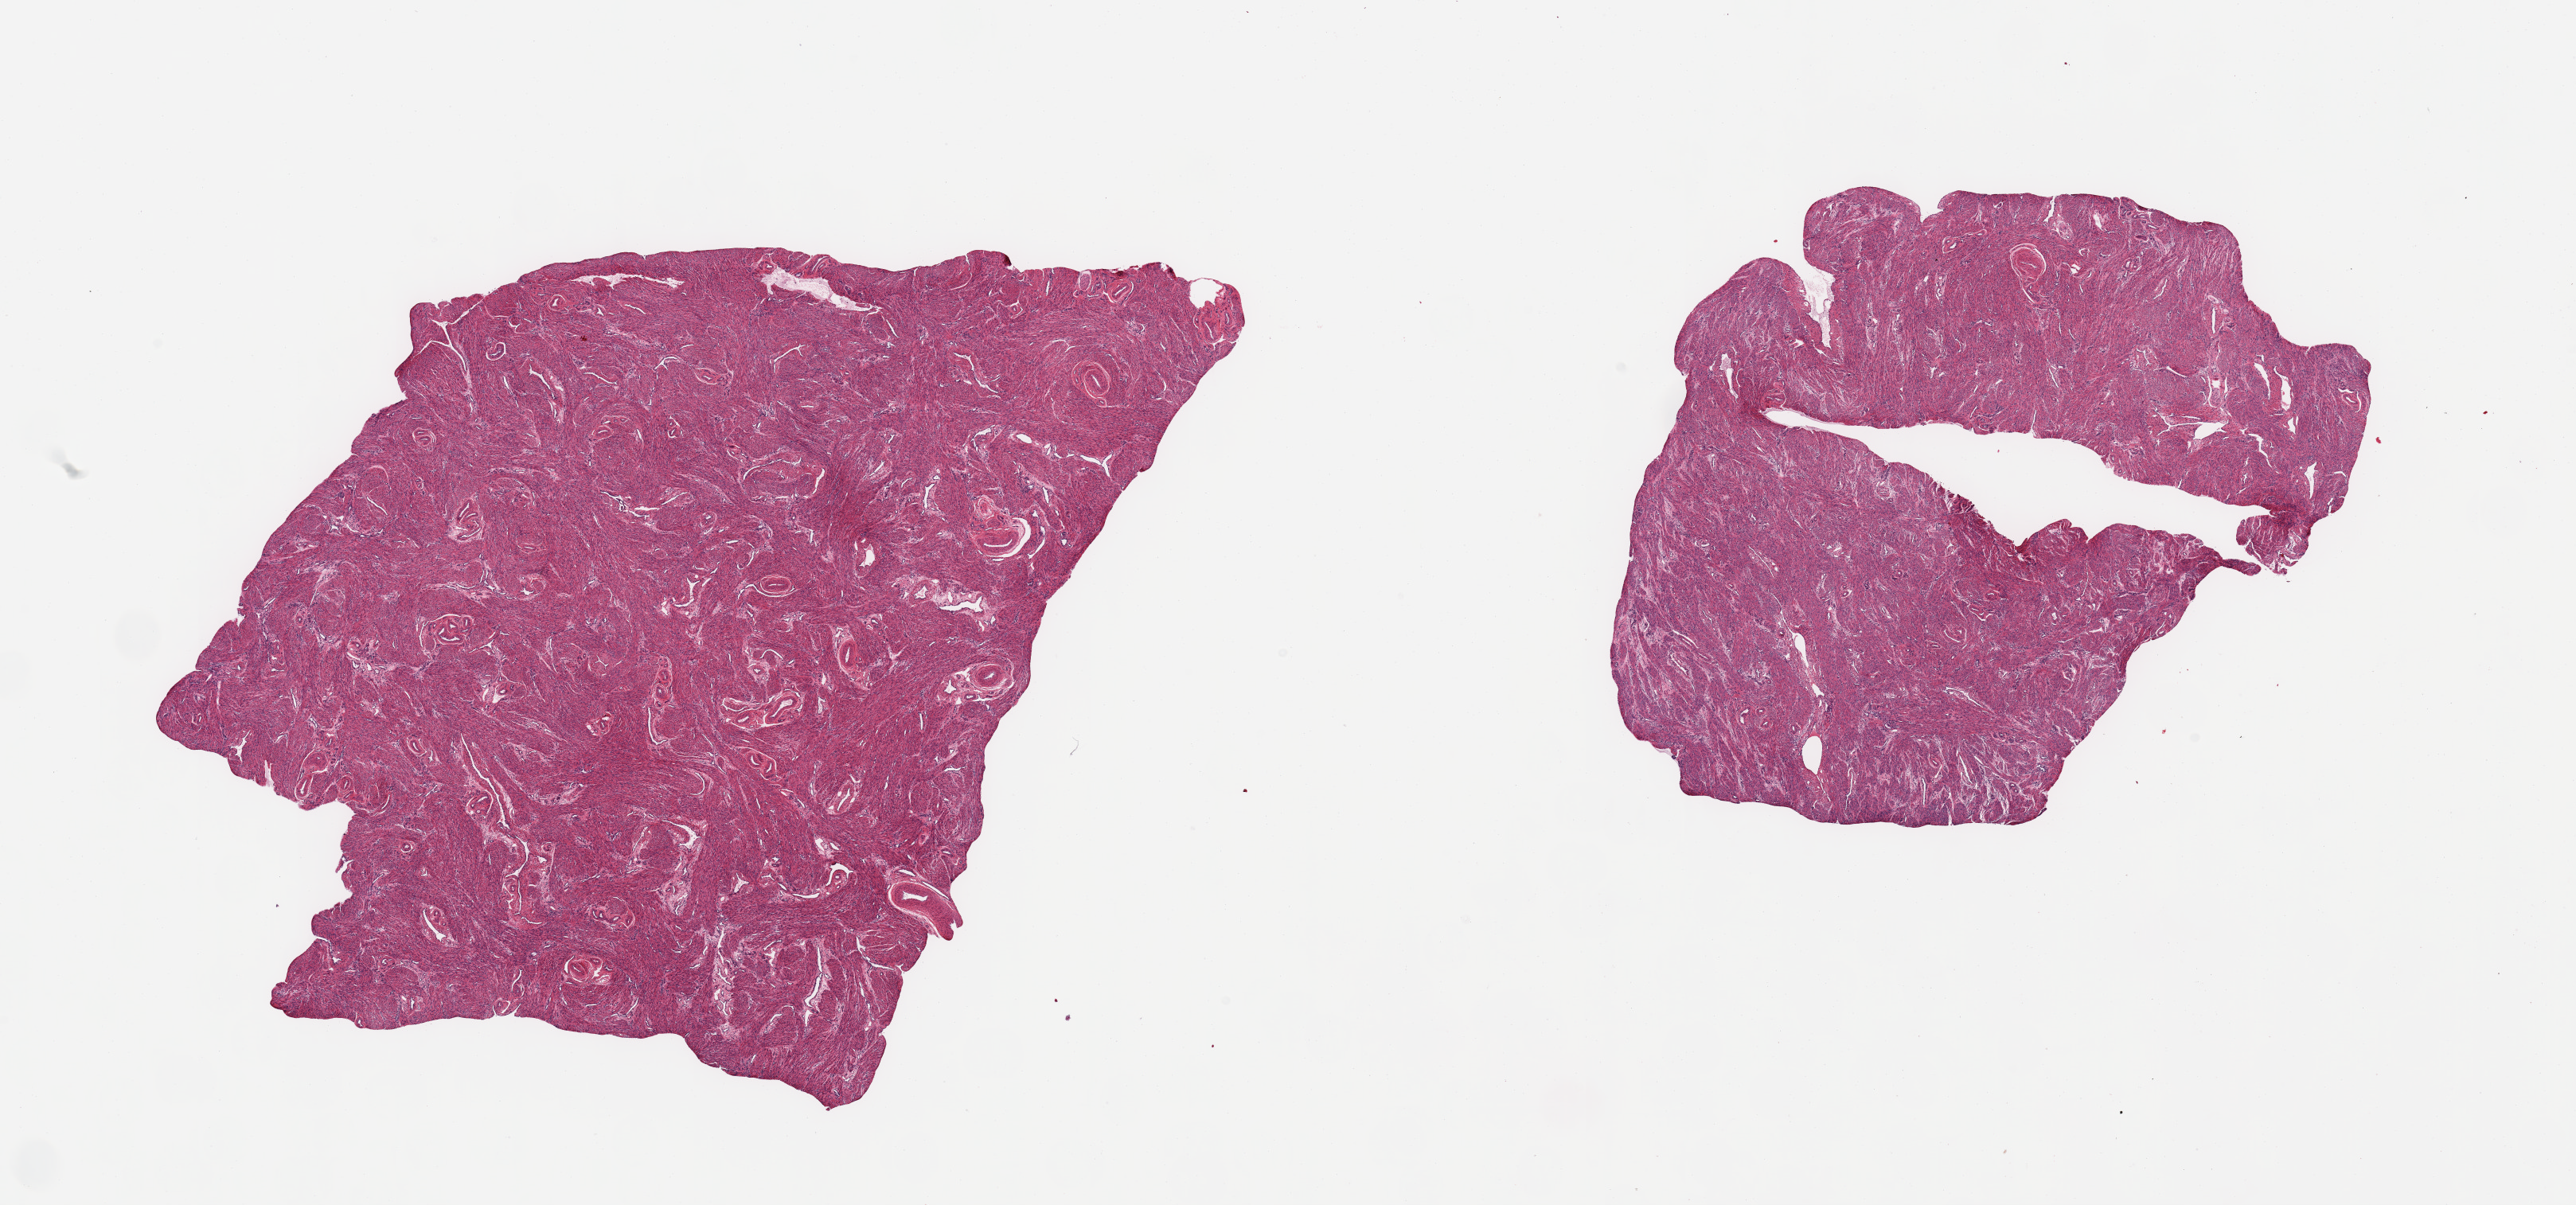
Hematoxylin and eosin (H&E) whole-slide image — a low-resolution overview of the entire scanned area, about 25.6 x 12.0 mm (slide scanned at 20x), PAXgene-fixed, paraffin-embedded tissue, target tissue: uterus, donor tissue sample.
Pathologist's review note for this sample: 2 pieces; all myometrium.